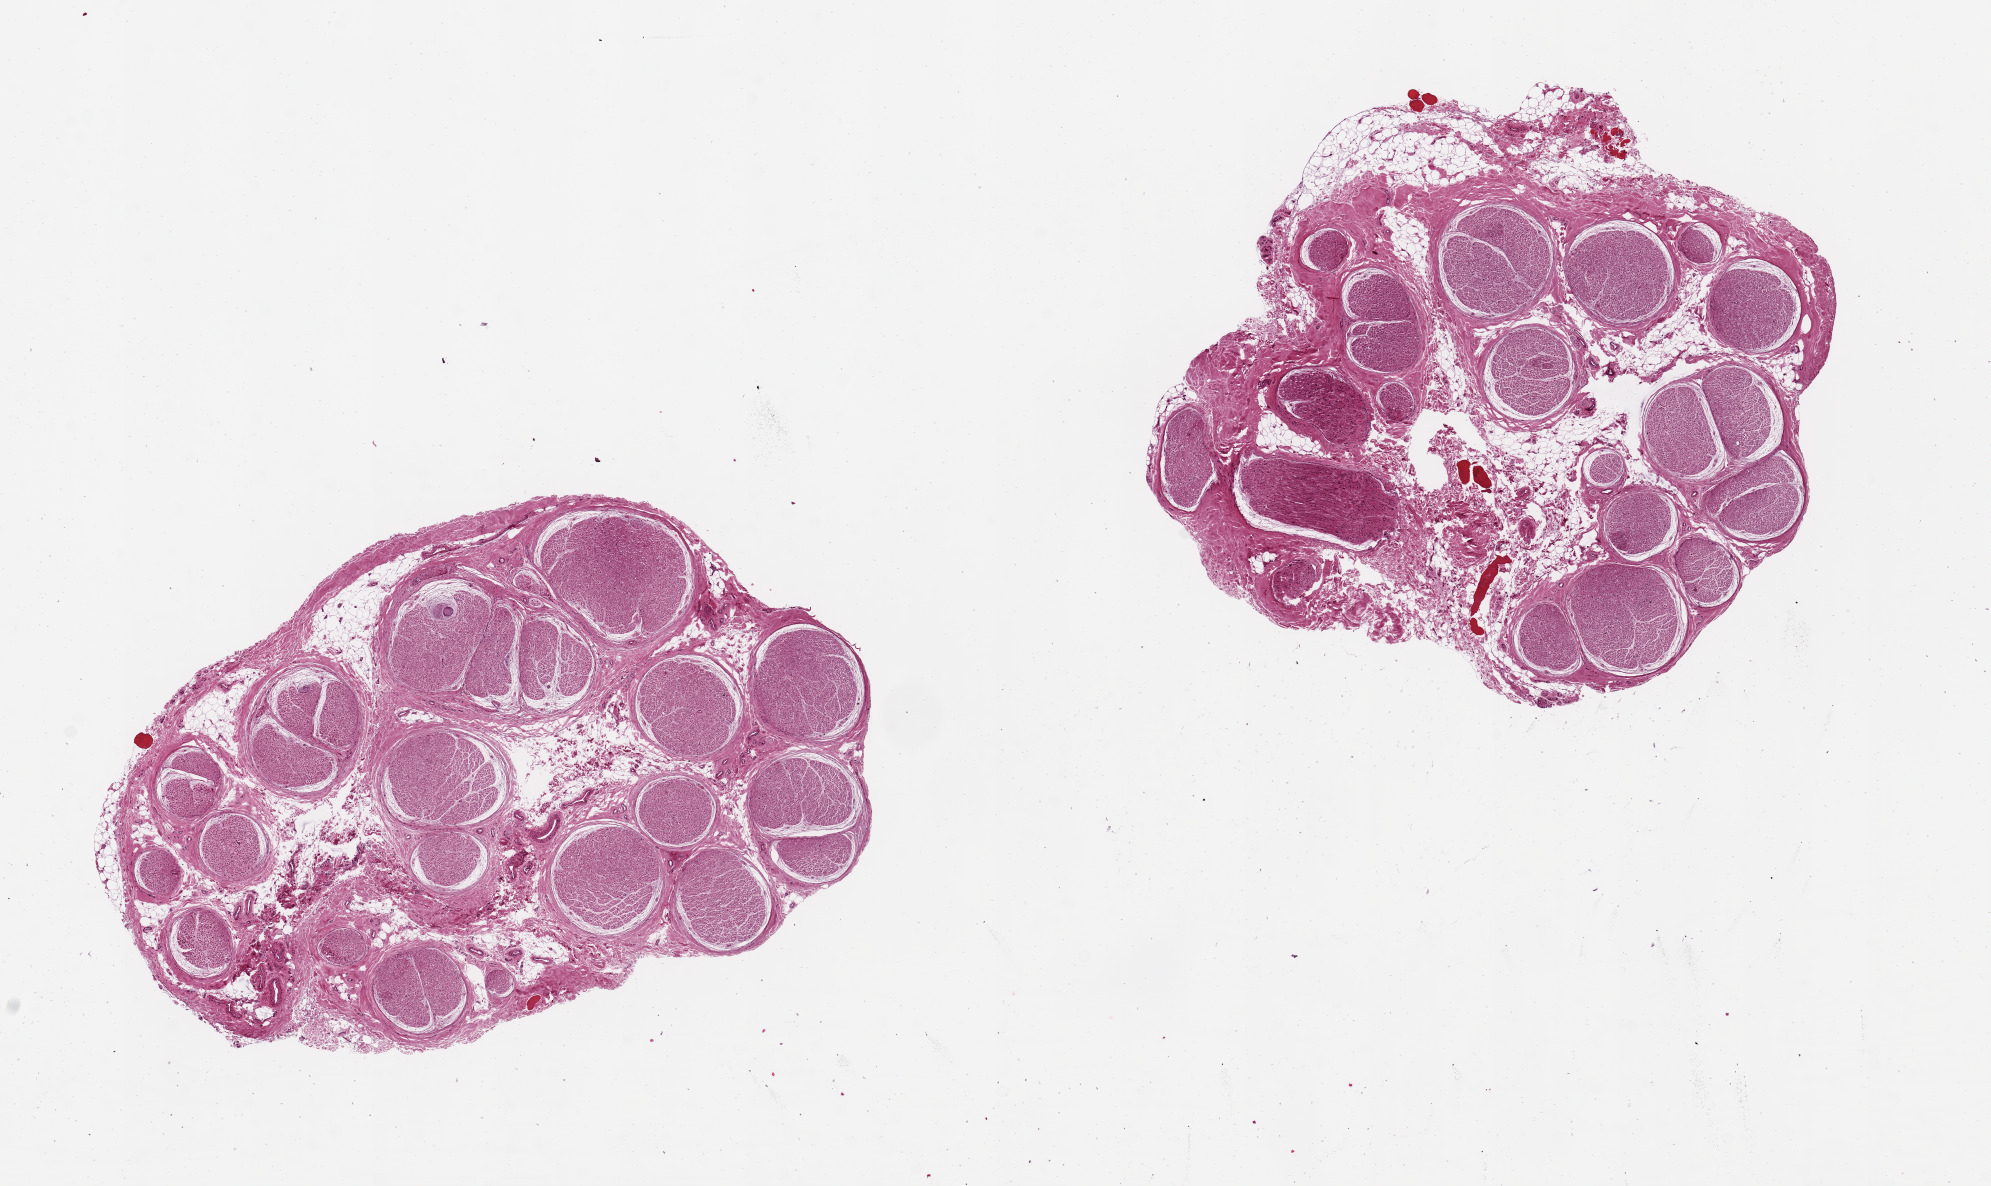
H&E whole-slide image — low-resolution overview of the scanned area, about 15.8 x 9.4 mm (from a 20x scan), PAXgene-fixed, paraffin-embedded tissue, target tissue: tibial nerve, tissue donor sample.
* reviewer comment on this tissue sample: 2 ~6x4mm aliquots, ~10% interstitial fat